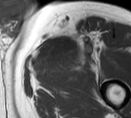
MRI of an extremity soft-tissue mass, one axial slice; position 55 of 55 along the scan axis; MR volume resampled by the dataset authors to the PET/CT grid (not the native acquisition matrix); 3.27 mm slice thickness; 131 × 118 image matrix, field of view 128 × 115 mm. Male patient. Case-level facts recorded for this patient, not image findings: histological type: pleiomorphic liposarcoma; grade: high; site of the primary tumour: left thigh.
Structures marked on this image (expert contour drawn on MRI and transferred to this co-registered scan by the dataset authors):
- gross tumour volume including surrounding oedema: box from (x=34, y=30) to (x=95, y=65) px
- gross tumour volume (mass): (x=34, y=37)–(x=69, y=63)